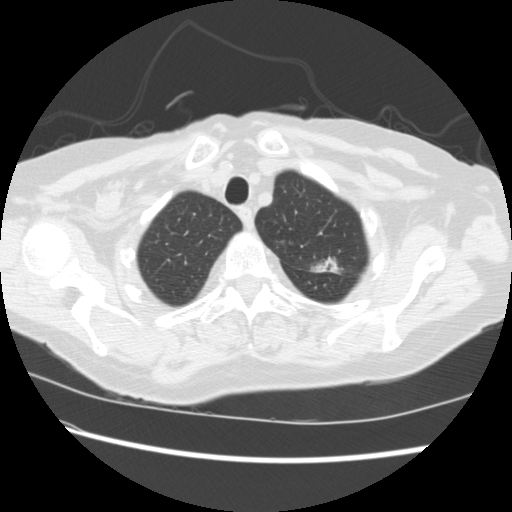
Chest CT (low-dose screening protocol), one axial image, baseline annual screen, lung window (W 1500 / L -600 HU), 2.5 mm slice thickness, standard (soft-tissue) reconstruction kernel (STANDARD), 120 kVp, 512 × 512 image matrix. Female participant, aged 74 years at enrolment. Former smoker at enrolment.
Expert reader's lesion annotation, bounding box <298,248,348,285> (left, top, right, bottom; pixels). The screening reader recorded 2 non-calcified nodules or masses ≥4 mm on this exam (left upper lobe, right lower lobe); which of them this box marks is not recorded. Official screen result: positive, change unspecified: nodule(s) >= 4 mm or enlarging nodule(s), mass(es), or other non-specific abnormalities suspicious for lung cancer. Later outcome: lung cancer diagnosed 309 days after this screen — non-small cell carcinoma, left upper lobe, stage IV (AJCC 6th edition).